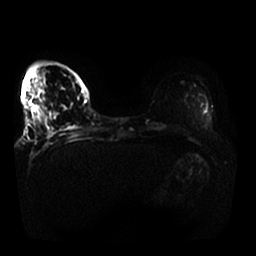
Breast MRI, one axial slice; slice 6 of 25 in the series (ordered by position); diffusion-weighted series; image 2 of 4 stored at this slice position (different b-values; order by instance number); 1.5 T; 4 mm slice thickness; 256 × 256 image matrix, field of view 370 × 370 mm. Female patient.
Annotated regions visible in this slice (manually delineated by an expert):
- tumour on diffusion-weighted imaging: box from (x=29, y=84) to (x=43, y=127) px